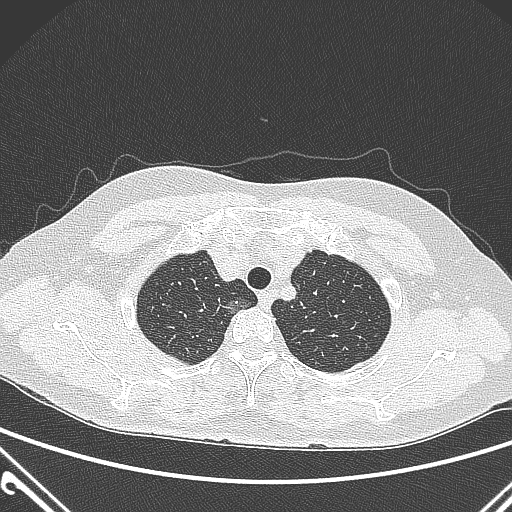
Chest CT, one axial slice; slice 242 of 300 in the series (ordered by position); 120 kVp; lung window (W 1500 / L -600 HU); 1 mm slice thickness; 512 × 512 image matrix, field of view 350 × 350 mm. Female patient, age 54 years. From the clinical record (not read from this slice): clinical TNM (as recorded): T1a N0 M0; histopathological grade: G1.
Annotated regions visible in this slice (bounding box drawn by a radiologist):
- lung tumour (recorded histology: adenocarcinoma): box from (x=221, y=289) to (x=254, y=324) px